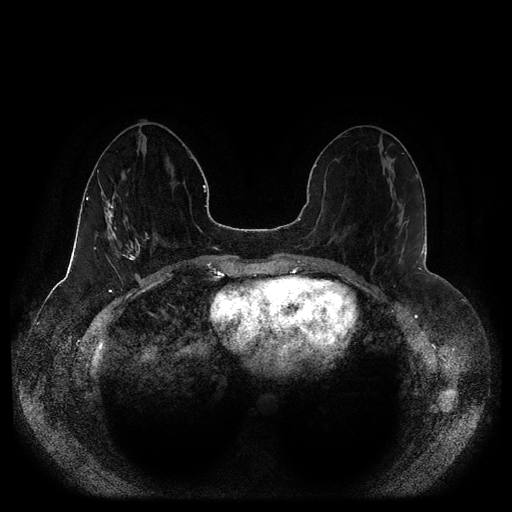
Breast MRI (dynamic contrast-enhanced, multi-phase), one axial slice. Dynamic contrast-enhanced series, time point 2 of 5 at this slice position (early post-contrast). 1.5 T. TE 2.5 ms, TR 5.2 ms. 2 mm slice thickness. 512 × 512 image matrix. Patient: female, 44 years.
Structures marked on this image (semi-automatic segmentation, software-assisted and operator-edited):
- breast lesion (labelled 'tumour' in the annotation; benign lesions carry a separate 'benign' label): bounding box (x1, y1, x2, y2) in pixels: (120, 243, 139, 260)
- breast lesion (labelled 'tumour' in the annotation; benign lesions carry a separate 'benign' label): (97, 169, 117, 245)